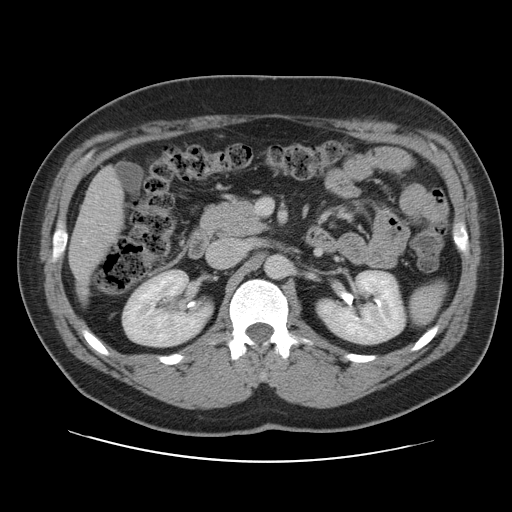
Contrast-enhanced abdominal CT, one axial slice. Slice 53 of 109 in the series (ordered by position). 120 kVp. Intravenous contrast given. Soft-tissue window (W 400 / L 40 HU). 5 mm slice thickness. 512 × 512 image matrix. Male patient, age 35 years. From the clinical record (not read from this slice): diagnosis: colorectal cancer liver metastases, imaged before liver resection; multiple liver metastases: yes; largest metastasis: 2.8 cm; disease in both lobes: yes.
Structures marked on this image (expert manual segmentation):
- liver: bounding box (x1, y1, x2, y2) in pixels: (70, 170, 123, 298)
- planned liver remnant (the part of the liver to remain after resection): (70, 170, 123, 298)